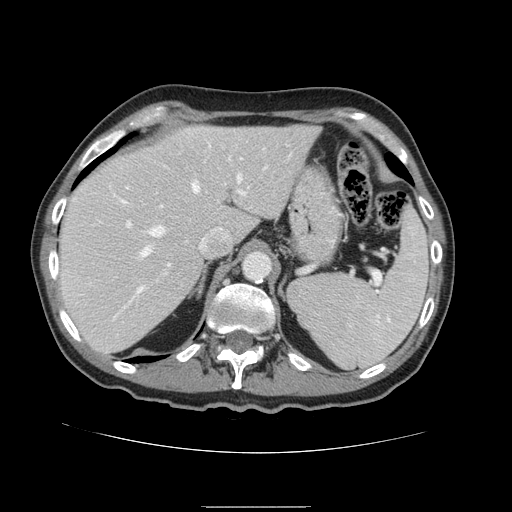
Contrast-enhanced abdominal CT, one axial slice. Slice 111 of 168 in the series (ordered by position). Intravenous contrast given. Soft-tissue window (W 400 / L 40 HU). 2.5 mm slice thickness. 512 × 512 image matrix, field of view 386 × 386 mm. Male patient, age 74 years. Case-level facts recorded for this patient, not image findings: diagnosis: colorectal cancer liver metastases, imaged before liver resection; multiple liver metastases: no; largest metastasis: 14.5 cm; disease in both lobes: yes.
Structures marked on this image (expert manual segmentation):
- hepatic veins: bounding box [x1, y1, x2, y2] px = [142, 175, 242, 255]
- liver: [59, 126, 320, 353]
- planned liver remnant (the part of the liver to remain after resection): [60, 126, 320, 353]
- portal vein (with intrahepatic branches): [95, 190, 246, 303]